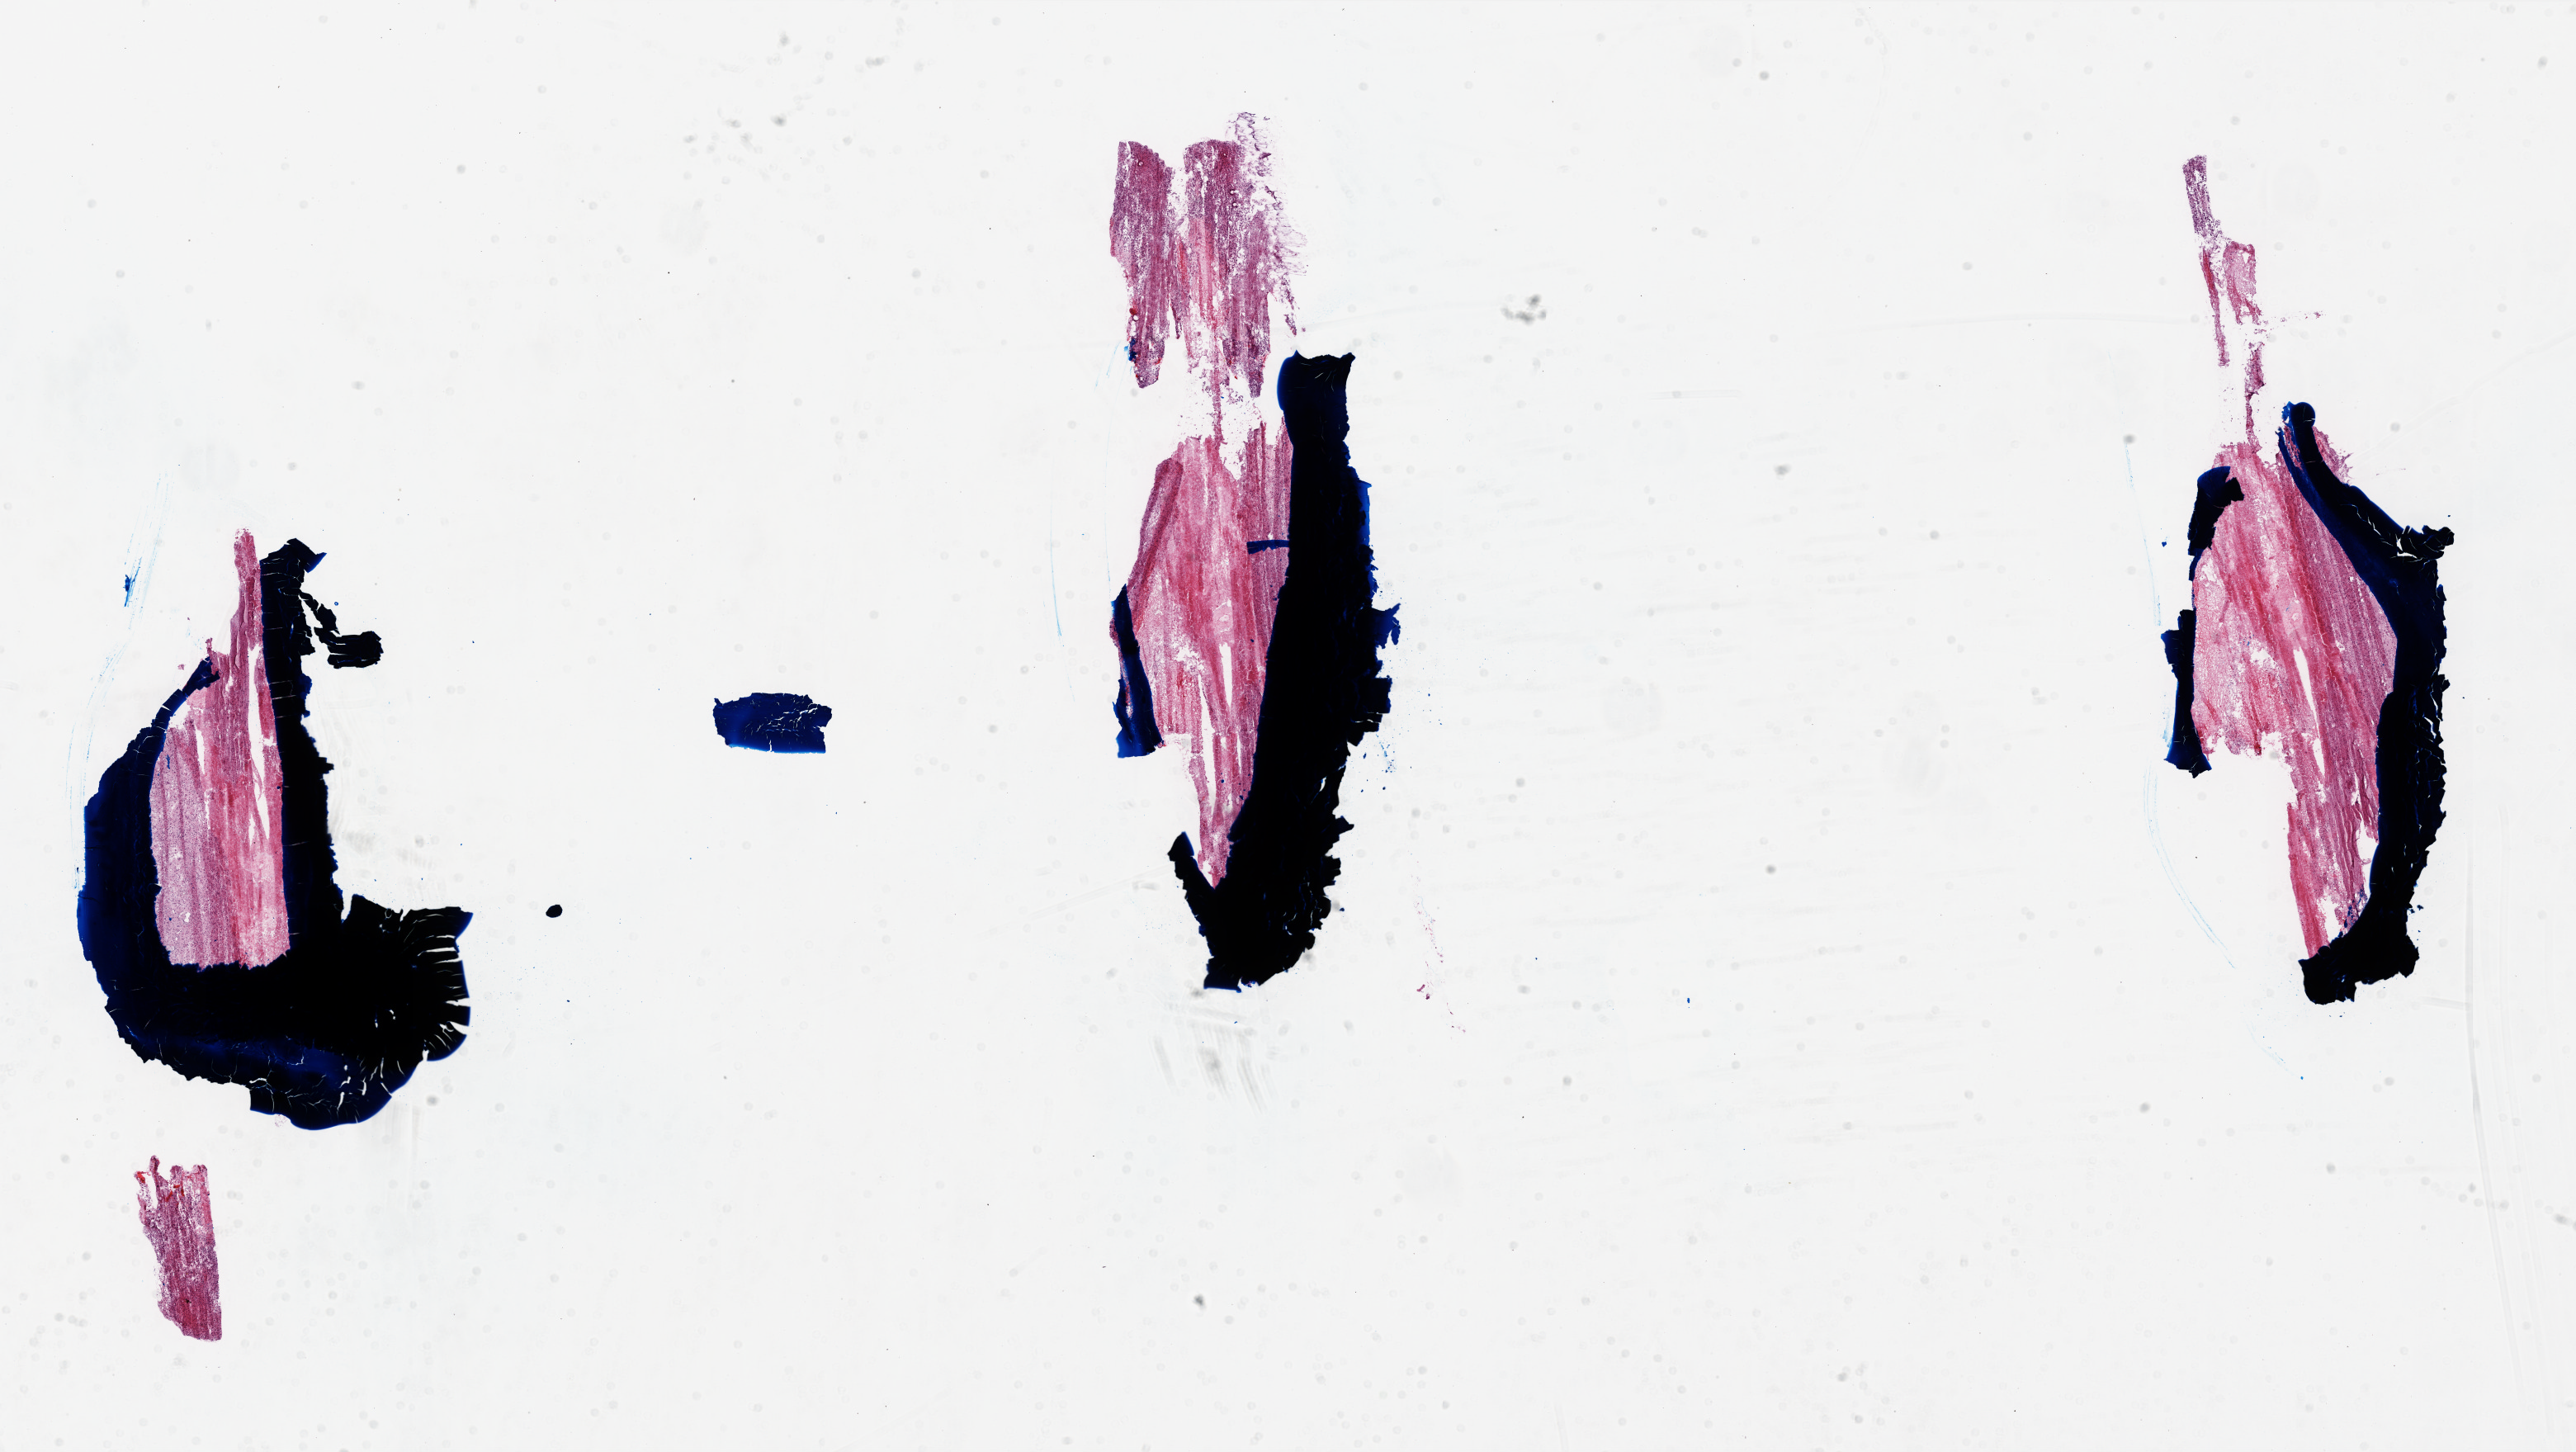
Hematoxylin and eosin (H&E) stained whole-slide image, a low-resolution overview of the entire scanned area, about 25.0 x 14.1 mm, frozen section from the top of the tissue portion, brain, primary tumour sample. Patient: male, age at initial diagnosis 74 years. Pathologist review of this section (percent, as recorded): tumour cells 20%, tumour nuclei 100%, normal cells 0%, stromal cells 0%, necrosis 80%.
• histologic diagnosis: Glioblastoma